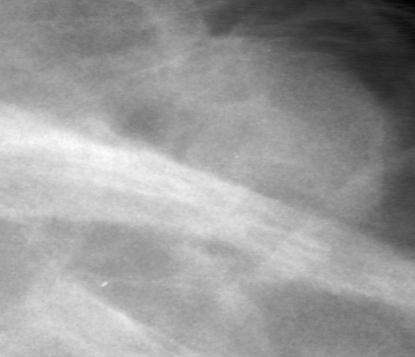
Cropped region of a digitized screen-film mammogram centred on a radiologist-marked abnormality, left breast, MLO view, BI-RADS breast density category 2 (scale 1–4).
Mass, shape lobulated, margins obscured; BI-RADS assessment category 0; subtlety rating 3 on a 1 (subtle) to 5 (obvious) scale; pathology (as recorded): benign.